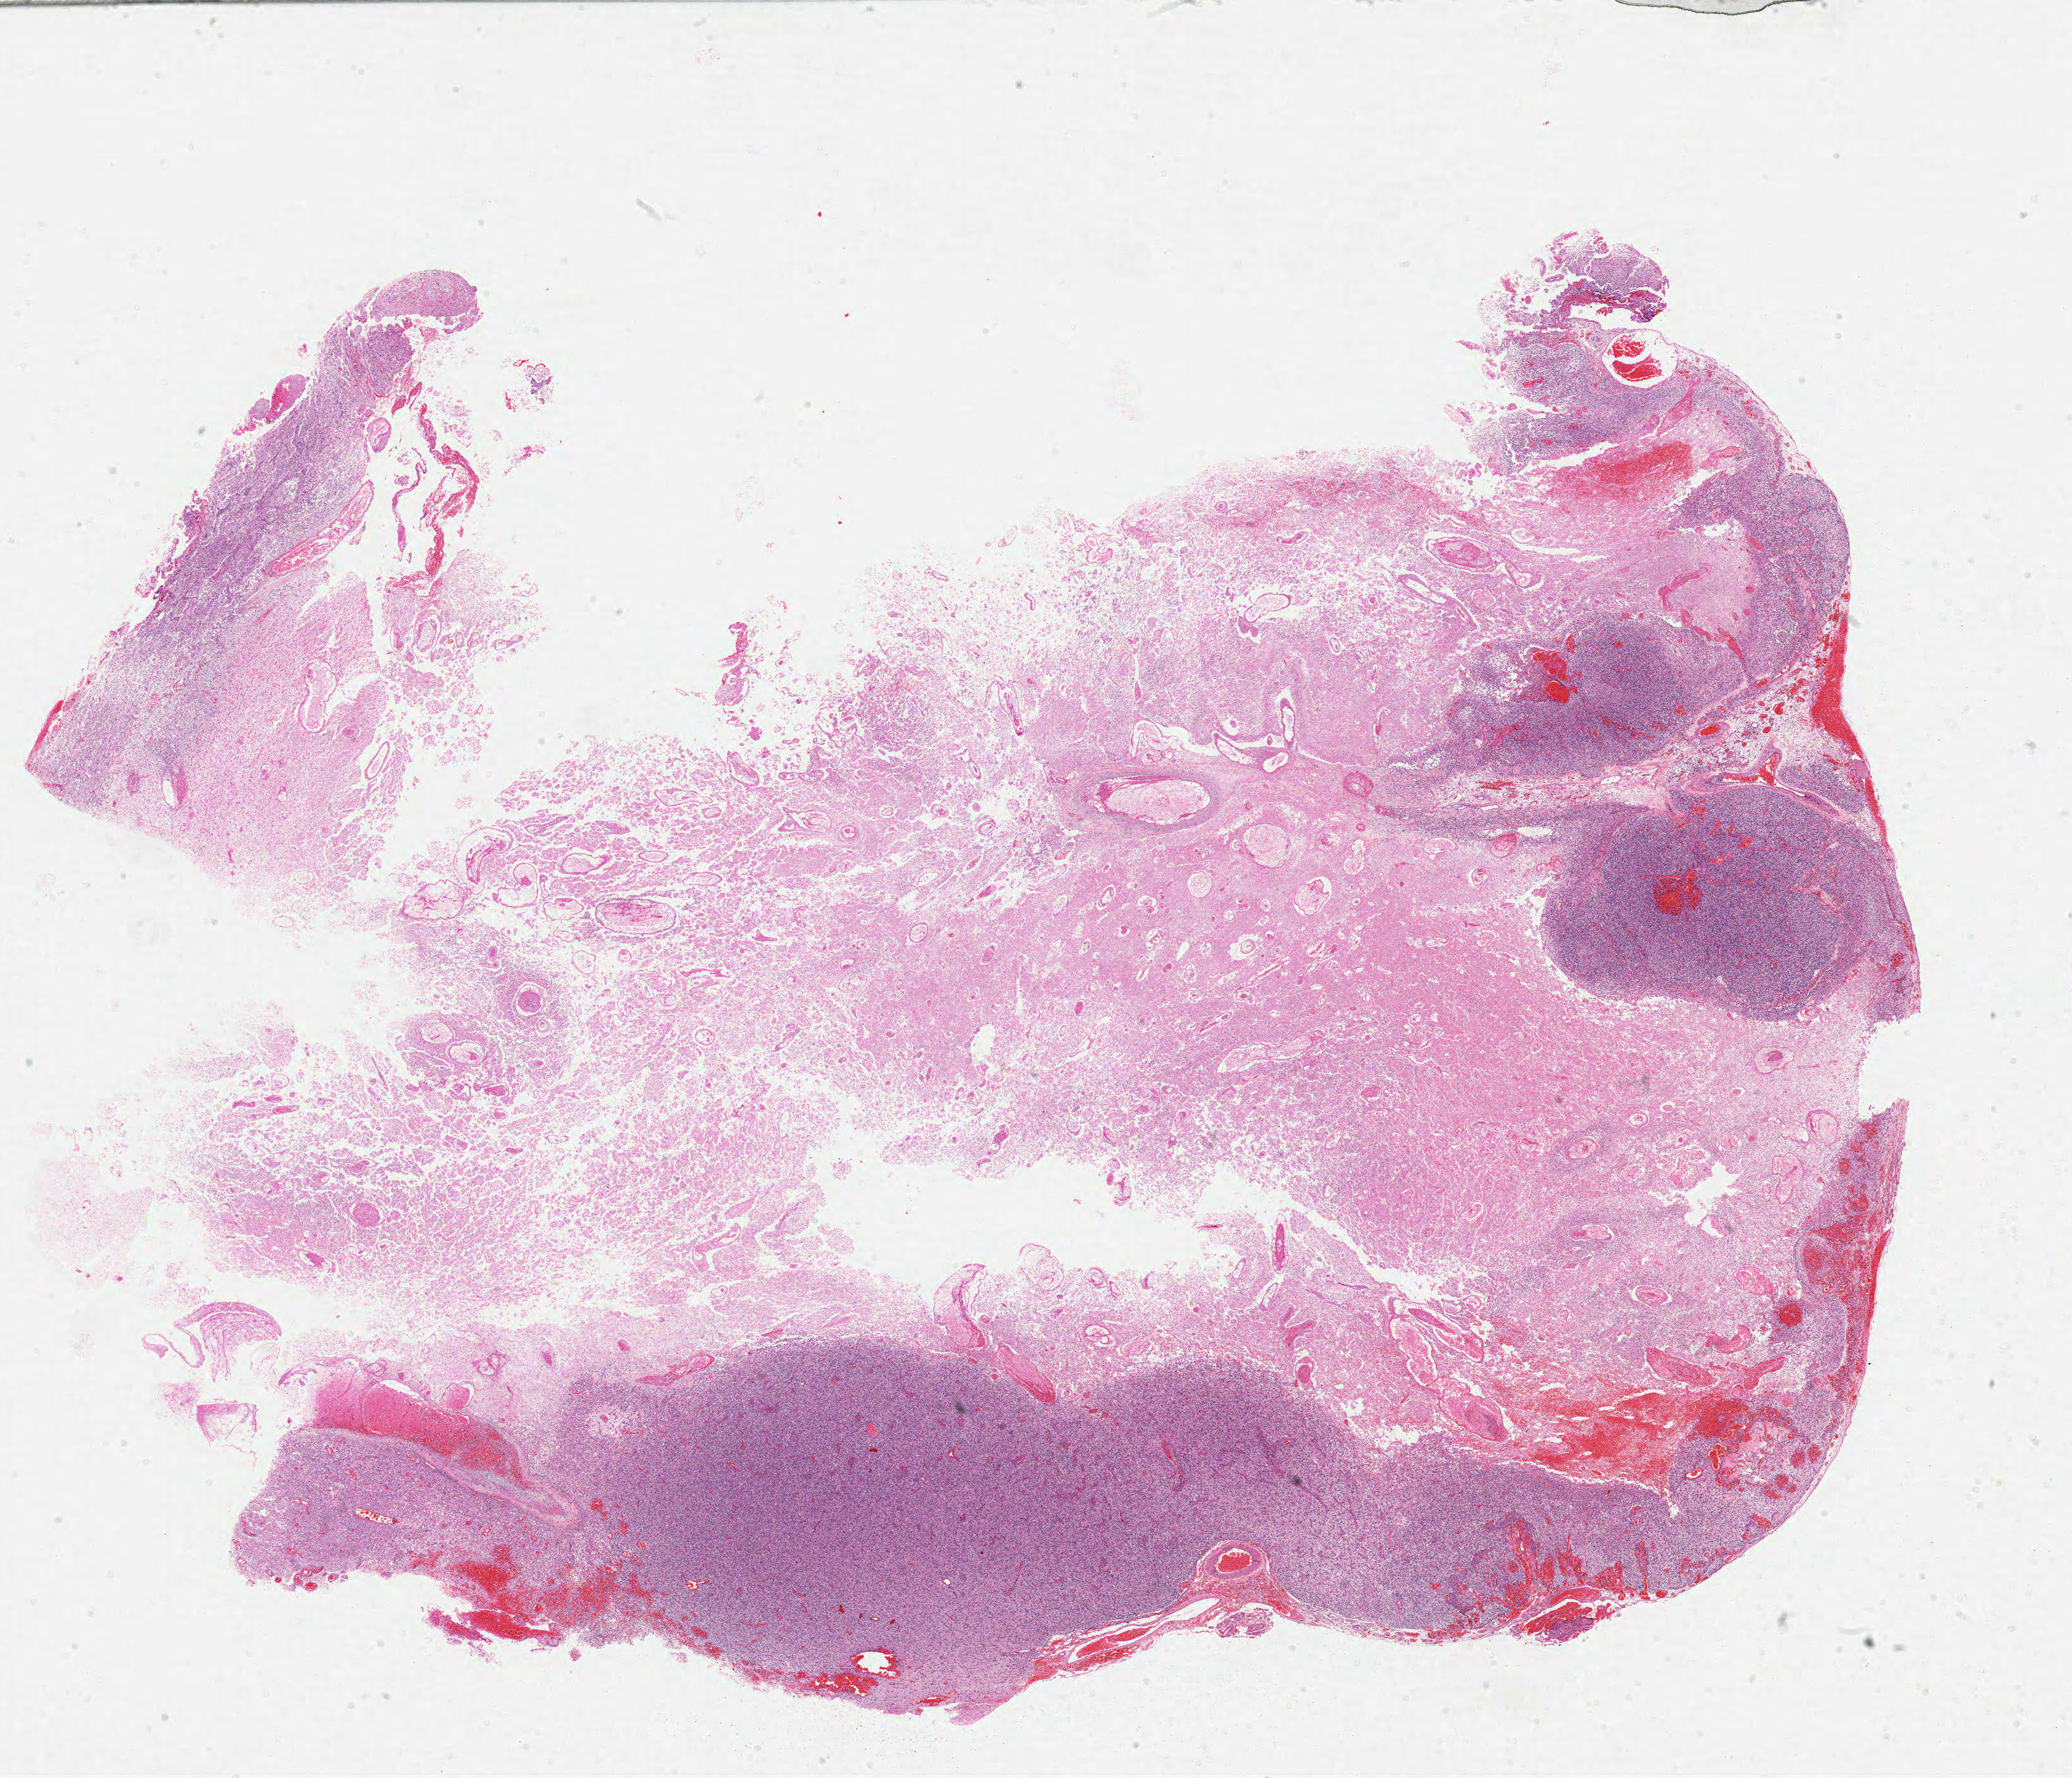
Digitized H&E tissue section (whole slide) — shown as a low-resolution overview of the whole scanned area (about 26.0 x 22.3 mm, acquisition: 20x scan). Formalin-fixed paraffin-embedded (FFPE) diagnostic section. Brain, primary tumour sample. Patient: male, age at initial diagnosis 74 years.
Pathologic diagnosis: Glioblastoma.